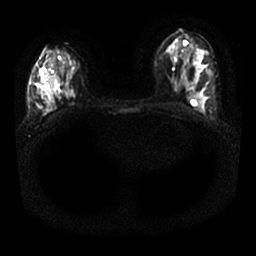
Breast MRI, one axial slice; slice 10 of 25 in the series (ordered by position); diffusion-weighted series; image 2 of 4 stored at this slice position (different b-values; order by instance number); 1.5 T; 4 mm slice thickness; 256 × 256 image matrix. Female patient.
Annotated regions visible in this slice (manually delineated by an expert):
- tumour on diffusion-weighted imaging: bounding box (x1, y1, x2, y2) in pixels: (66, 92, 73, 98)